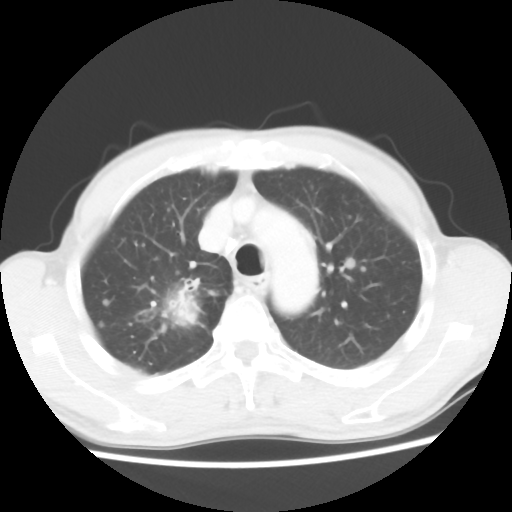
Chest CT, one axial slice; slice 40 of 52 in the series (ordered by position); reconstruction kernel STANDARD; 100 kVp; lung window (W 1500 / L -600 HU); 512 × 512 image matrix, field of view 323 × 323 mm. Patient: male, 66 years. Case-level facts recorded for this patient, not image findings: clinical TNM (as recorded): T2 N0 M1a.
Outlined on this slice (bounding box drawn by a radiologist):
- lung tumour (recorded histology: adenocarcinoma): bounding box [x1, y1, x2, y2] px = [136, 271, 213, 343]